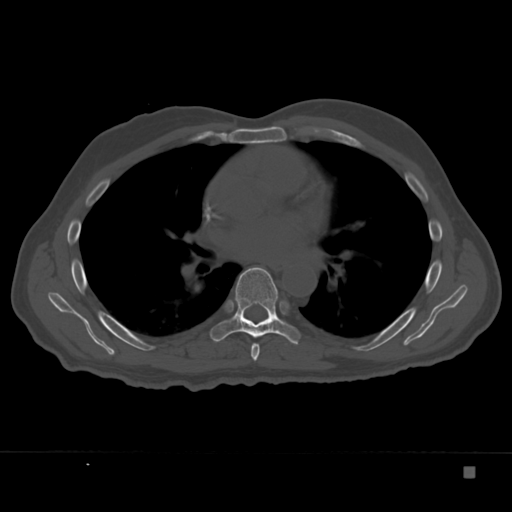
CT including the spine, one axial slice. Reconstruction kernel Br40s. 120 kVp. Bone window (W 1800 / L 400 HU). 512 × 512 image matrix, field of view 389 × 389 mm. Male patient, age 72 years. Case-level facts recorded for this patient, not image findings: primary cancer: skeletal.
Annotated regions visible in this slice (semi-automatic segmentation, software-assisted and operator-edited):
- T6 vertebra: bounding box [x1, y1, x2, y2] px = [251, 344, 260, 361]
- T7 vertebra: [210, 267, 300, 345]